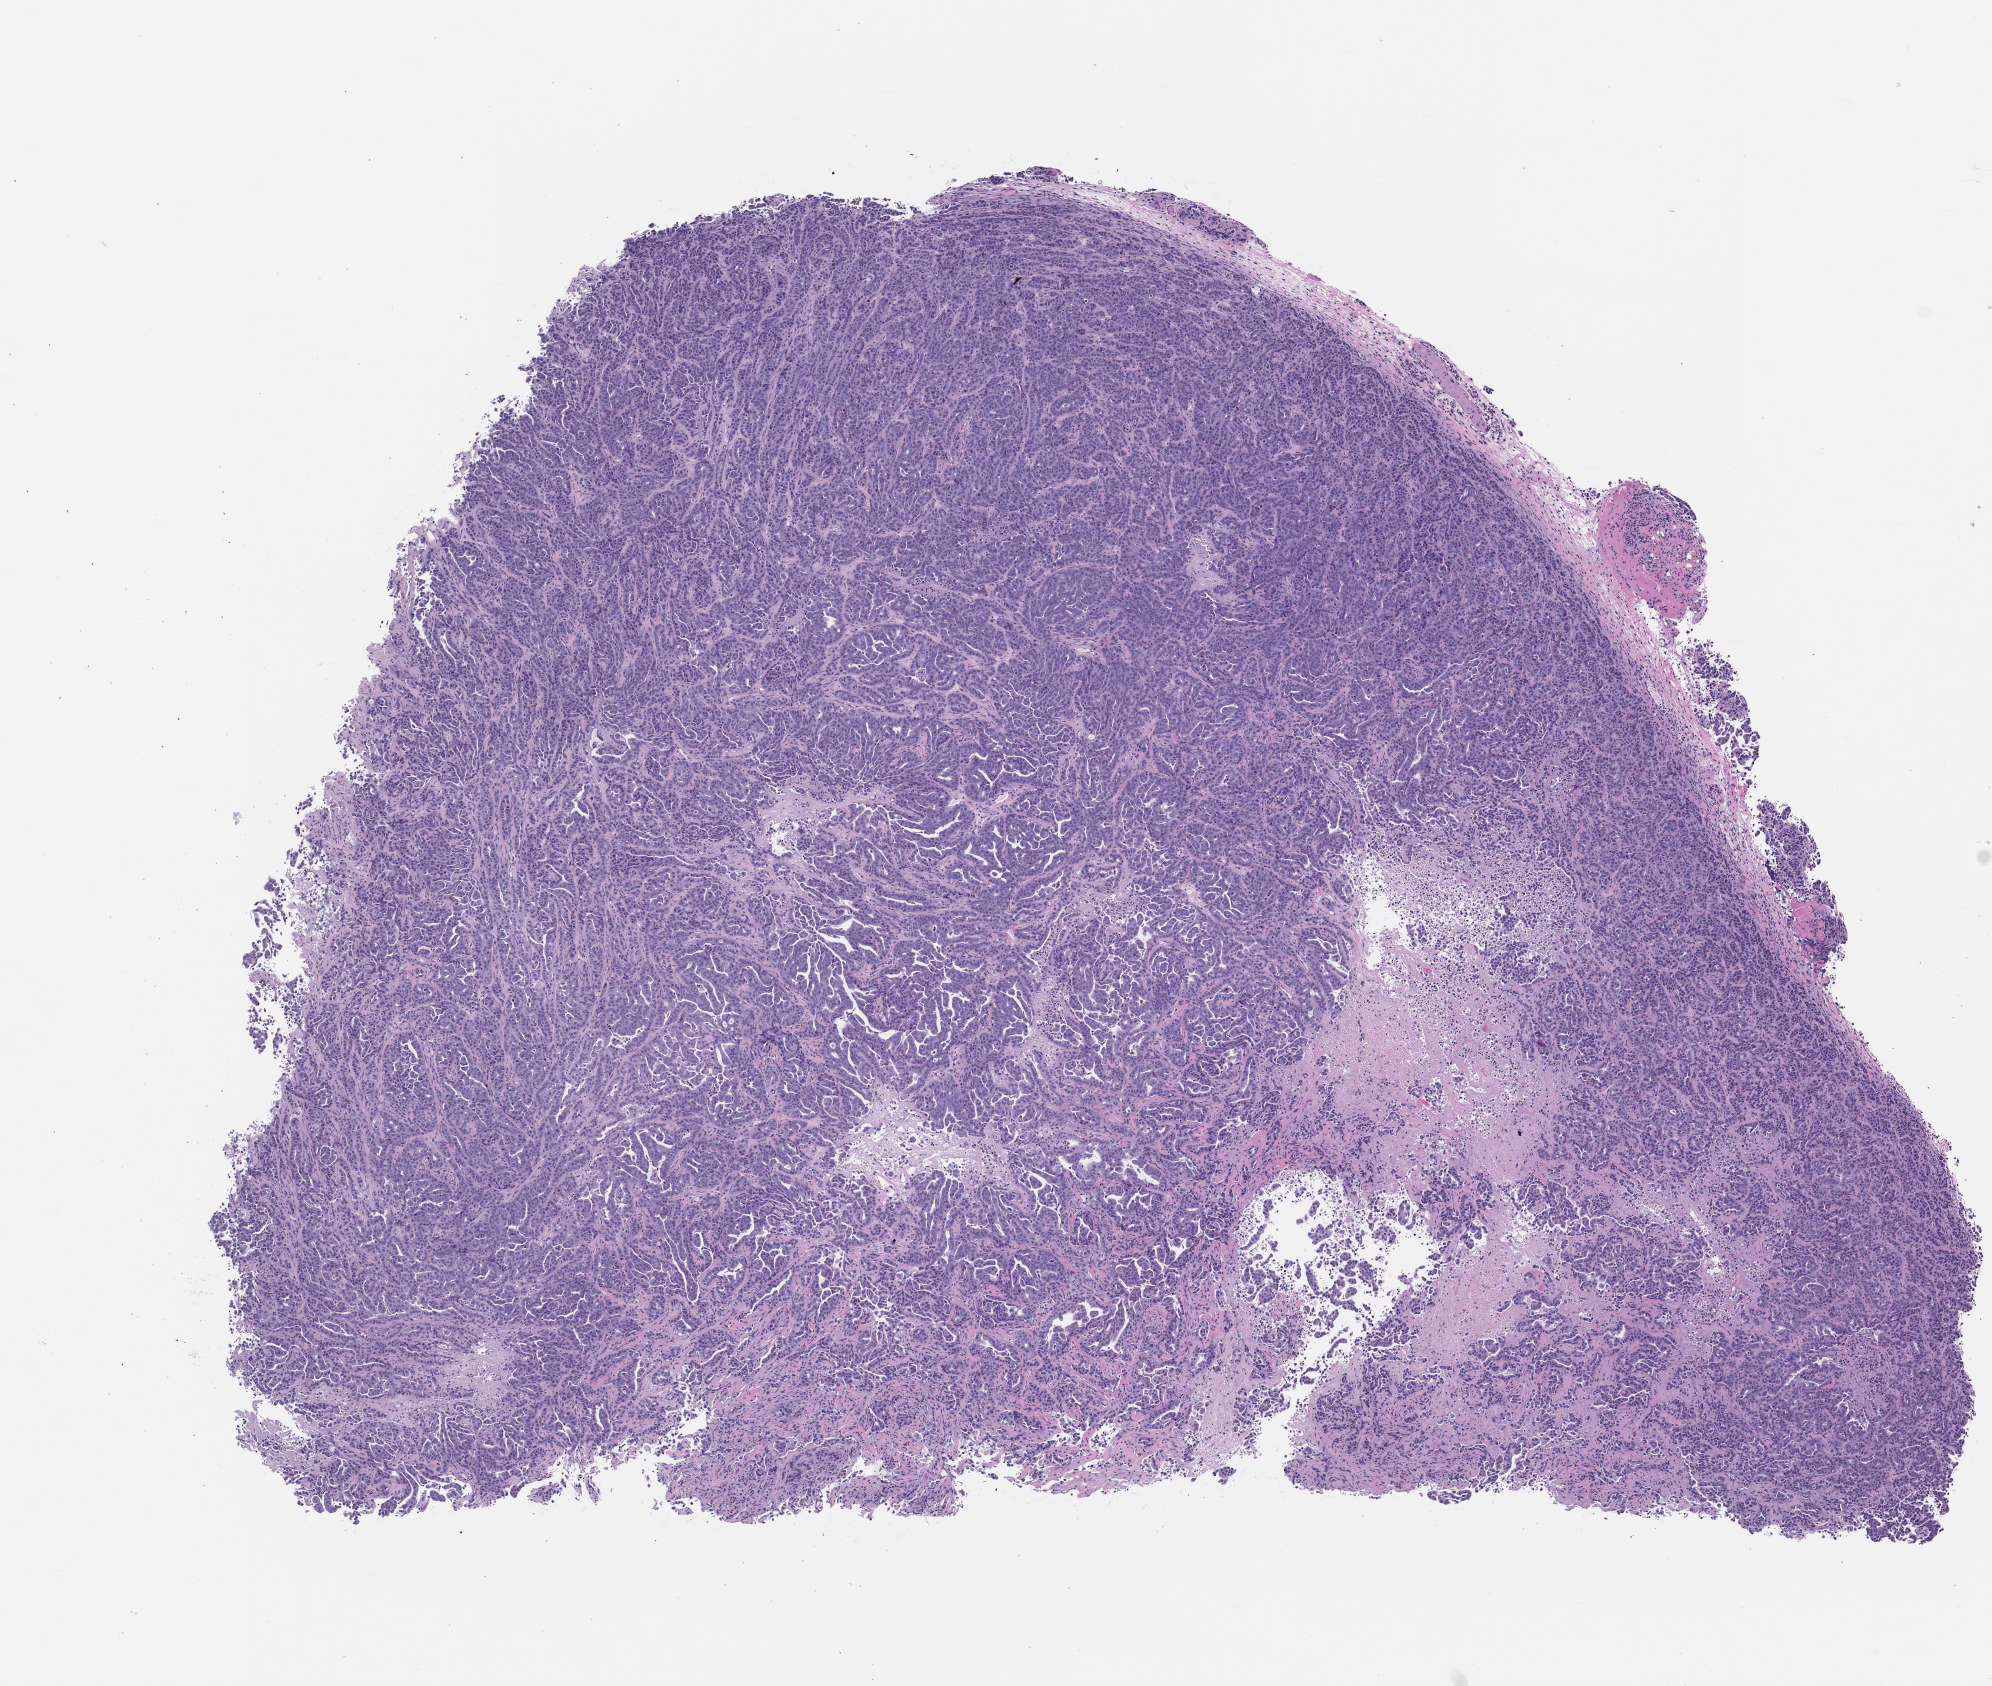
Haematoxylin and eosin whole-slide image of a patient-derived xenograft (PDX) tumor grown in a mouse, low-resolution overview of the scanned area, about 8.0 x 6.8 mm; formalin-fixed, paraffin-embedded (FFPE) tissue; originating tumor site category: lung.
Originating patient diagnosis: Lung Adenocarcinoma.